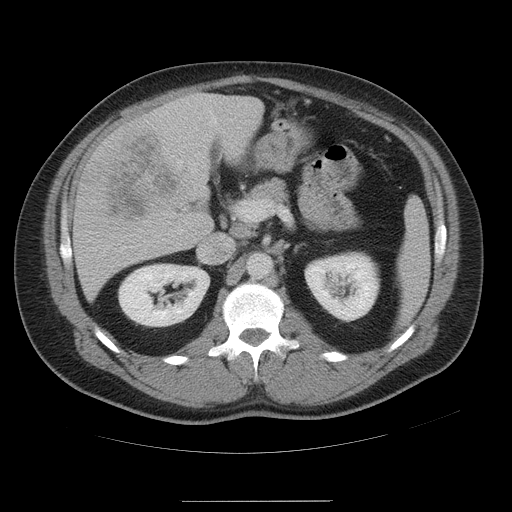
Contrast-enhanced abdominal CT, one axial slice; slice 27 of 54 in the series (ordered by position); 120 kVp; intravenous contrast given; soft-tissue window (W 400 / L 40 HU); 512 × 512 image matrix, field of view 436 × 436 mm. Male patient, age 40 years. Case-level facts recorded for this patient, not image findings: diagnosis: colorectal cancer liver metastases, imaged before liver resection; multiple liver metastases: no; largest metastasis: 15 cm; disease in both lobes: no.
Annotated regions visible in this slice (manually delineated by an expert):
- liver: bounding box <73,94,263,302> (left, top, right, bottom; pixels)
- planned liver remnant (the part of the liver to remain after resection): <215,95,263,156>
- liver metastasis: <96,118,209,228>